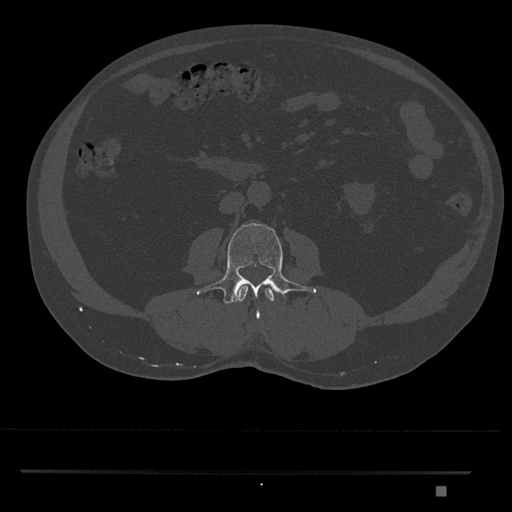
CT including the spine, one axial slice. Position 694 of 1134 along the scan axis. Reconstruction kernel Br40s/3. Bone window (W 1800 / L 400 HU). 0.5 mm slice thickness. 512 × 512 image matrix. Patient: male, 65 years. From the clinical record (not read from this slice): primary cancer: prostate.
Structures marked on this image (semi-automatically segmented with operator editing):
- L2 vertebra: box from (x=237, y=286) to (x=275, y=302) px
- L3 vertebra: (x=197, y=223)–(x=316, y=319)